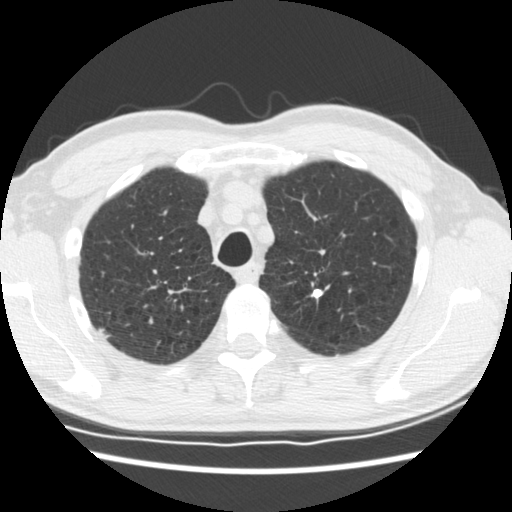
Low-dose screening chest CT, one axial slice. Position 145 of 183 along the scan axis. Reconstruction kernel STANDARD. 120 kVp. Lung window (W 1500 / L -600 HU). 2.5 mm slice thickness. 512 × 512 image matrix.
Annotated regions visible in this slice (outlined manually by an expert reader):
- lesion 2 (tumor, upper lobe of right lung): bounding box (x1, y1, x2, y2) in pixels: (100, 327, 113, 340)